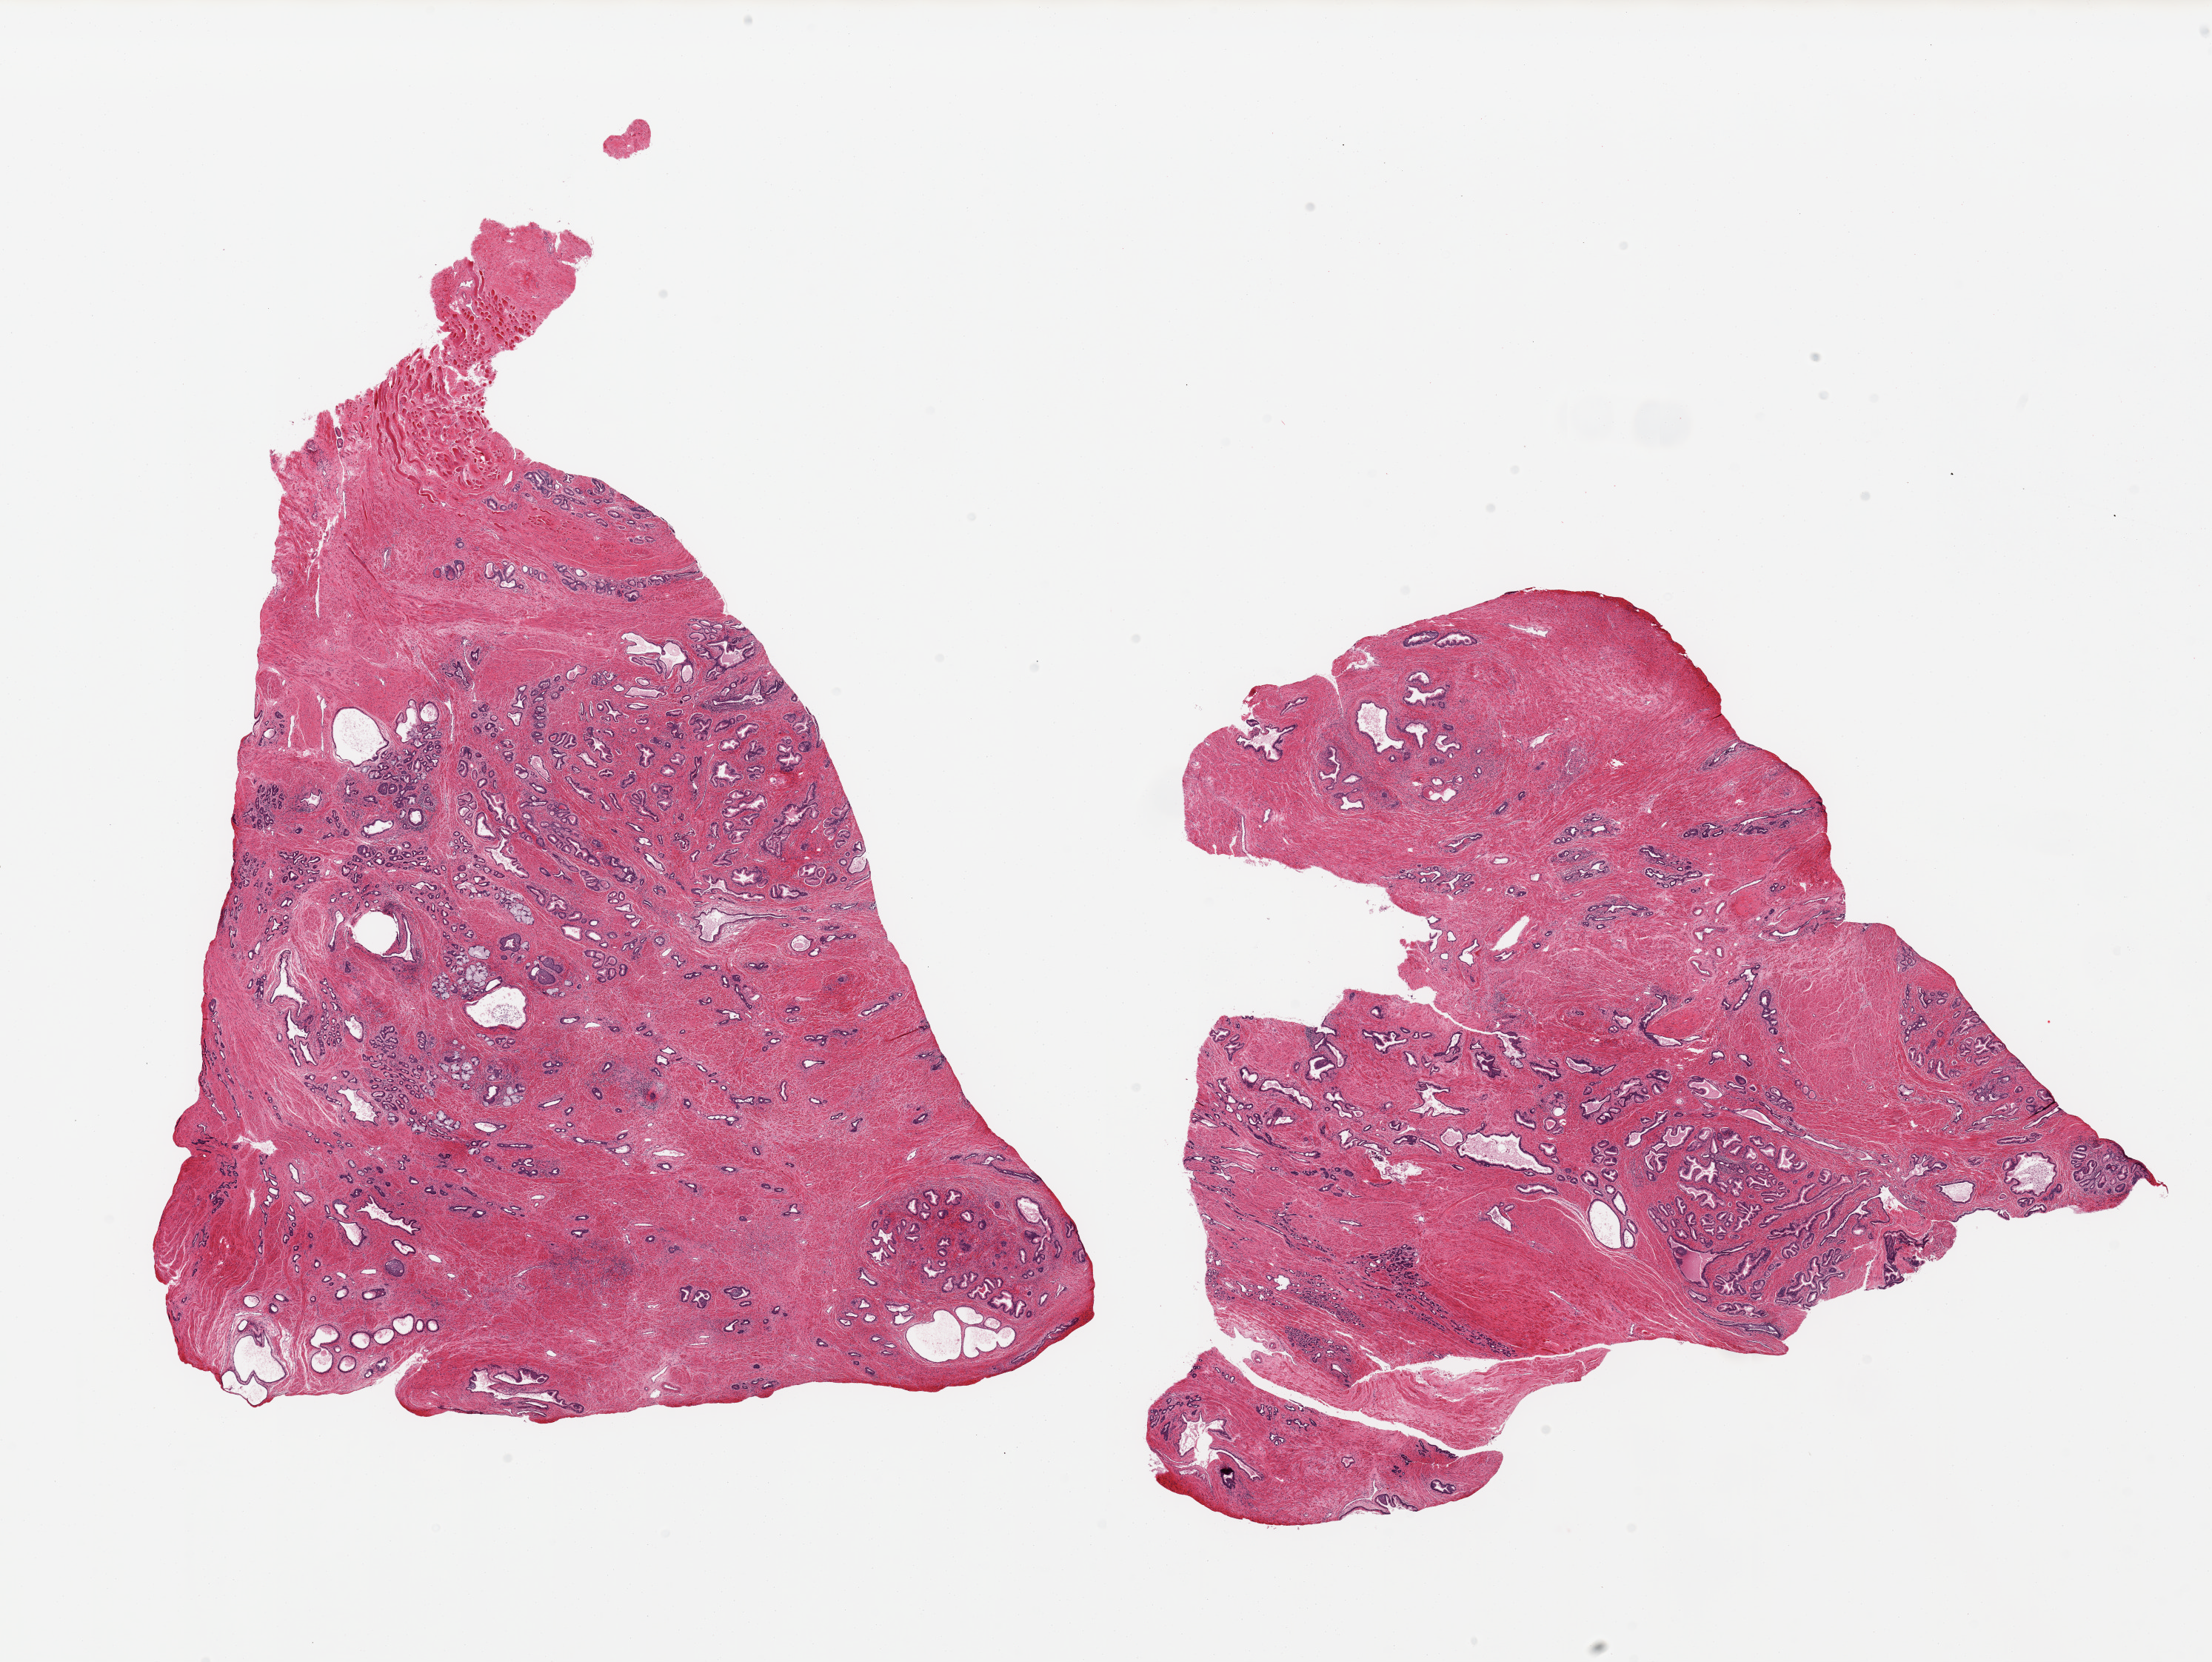
Whole-slide image, hematoxylin and eosin (H&E) stain, shown as a low-resolution overview of the whole scanned area (about 23.6 x 17.7 mm, slide scanned at 20x). PAXgene-fixed paraffin-embedded (PFPE) section. Section of prostate (target tissue). Tissue donor sample. Donor sex: male.
* review note (as recorded): 2 pieces